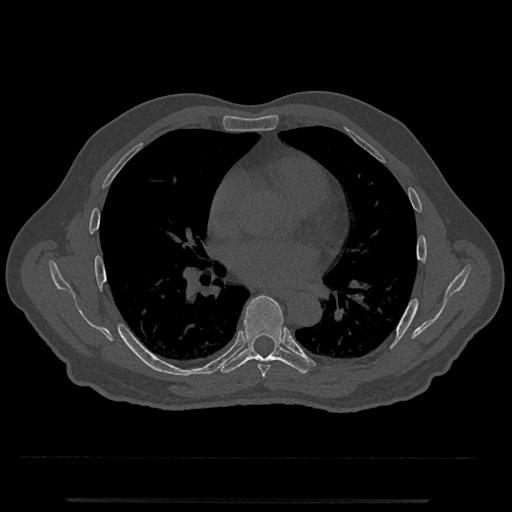
CT including the spine, one axial slice. Slice 703 of 797 in the series (ordered by position). Bone window (W 1800 / L 400 HU). 512 × 512 image matrix, field of view 419 × 419 mm. Patient: male, 63 years. Case-level facts recorded for this patient, not image findings: primary cancer: prostate.
Structures marked on this image (semi-automatic segmentation, software-assisted and operator-edited):
- T6 vertebra: box from (x=258, y=364) to (x=270, y=378) px
- T7 vertebra: (x=218, y=295)–(x=311, y=374)